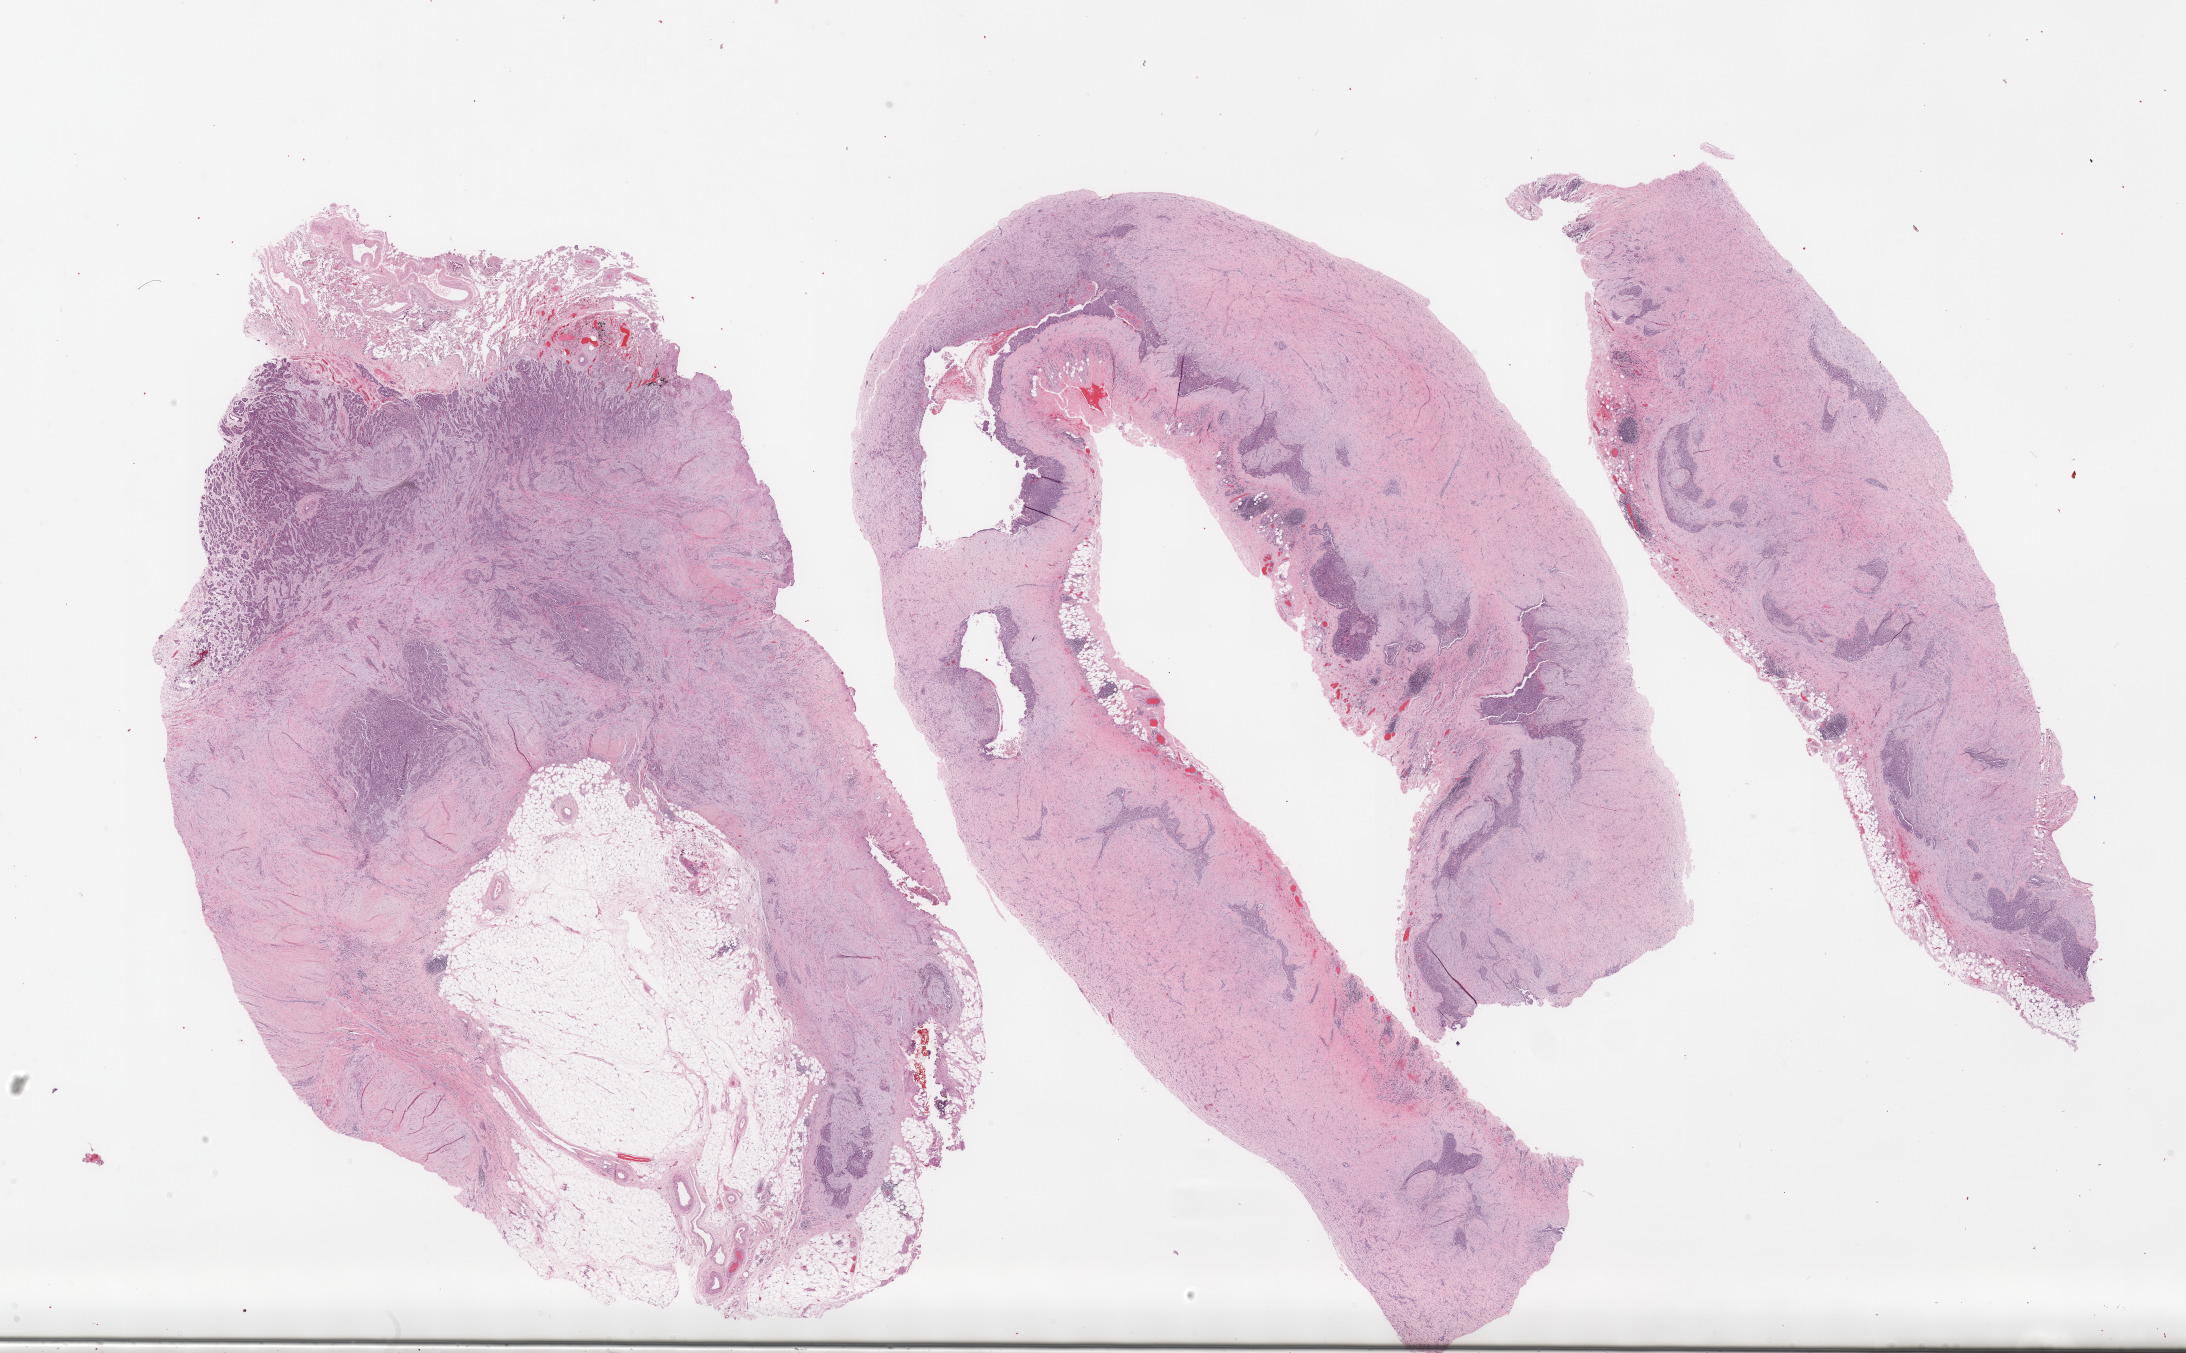
H&E-stained whole-slide image, low-resolution overview of the scanned area, about 35.1 x 21.7 mm; formalin-fixed paraffin-embedded (FFPE) diagnostic section; mesothelium, primary tumour sample. Male, age 76 years at initial diagnosis.
Diagnosis: Mesothelioma, biphasic, malignant (pleura, NOS). AJCC pathologic stage: III (7th edition).